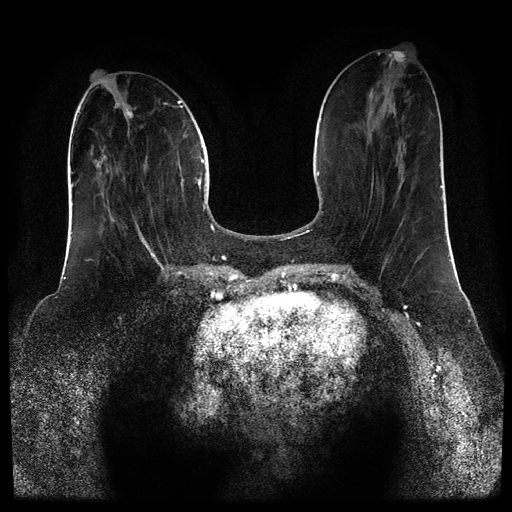
Breast MRI (dynamic contrast-enhanced, multi-phase), one axial slice; slice 33 of 110 in the series (ordered by position); dynamic contrast-enhanced series, time point 2 of 5 at this slice position (early post-contrast); 1.5 T; TE 2.6 ms, TR 5.4 ms; 512 × 512 image matrix, field of view 340 × 340 mm. Patient: female, 43 years.
Annotated regions visible in this slice (semi-automatically segmented with operator editing):
- breast lesion (labelled 'tumour' in the annotation; benign lesions carry a separate 'benign' label): bounding box (x1, y1, x2, y2) in pixels: (125, 106, 133, 119)